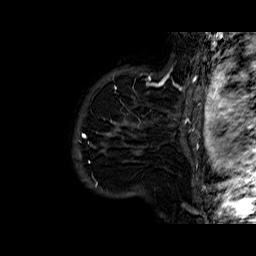
Breast MRI (dynamic contrast-enhanced), one sagittal slice. Dynamic contrast-enhanced series, time point 2 of 6 at this slice position (early post-contrast). 1.5 T. TE 6.4 ms, TR 32.8 ms. 4 mm slice thickness. 256 × 256 image matrix, field of view 200 × 200 mm. Female patient. From the clinical record (not read from this slice): setting: breast cancer imaged before/during neoadjuvant chemotherapy; receptor status: HR-positive, HER2-negative.
Annotated regions visible in this slice (semi-automatically segmented with operator editing):
- analysis volume of interest (the breast-tissue region the enhancement analysis was run in; not a lesion): bounding box (x1, y1, x2, y2) in pixels: (86, 77, 163, 177)
- tumour enhancement mask (voxels above the 100 % enhancement threshold inside the analysis volume of interest): (107, 81, 163, 135)